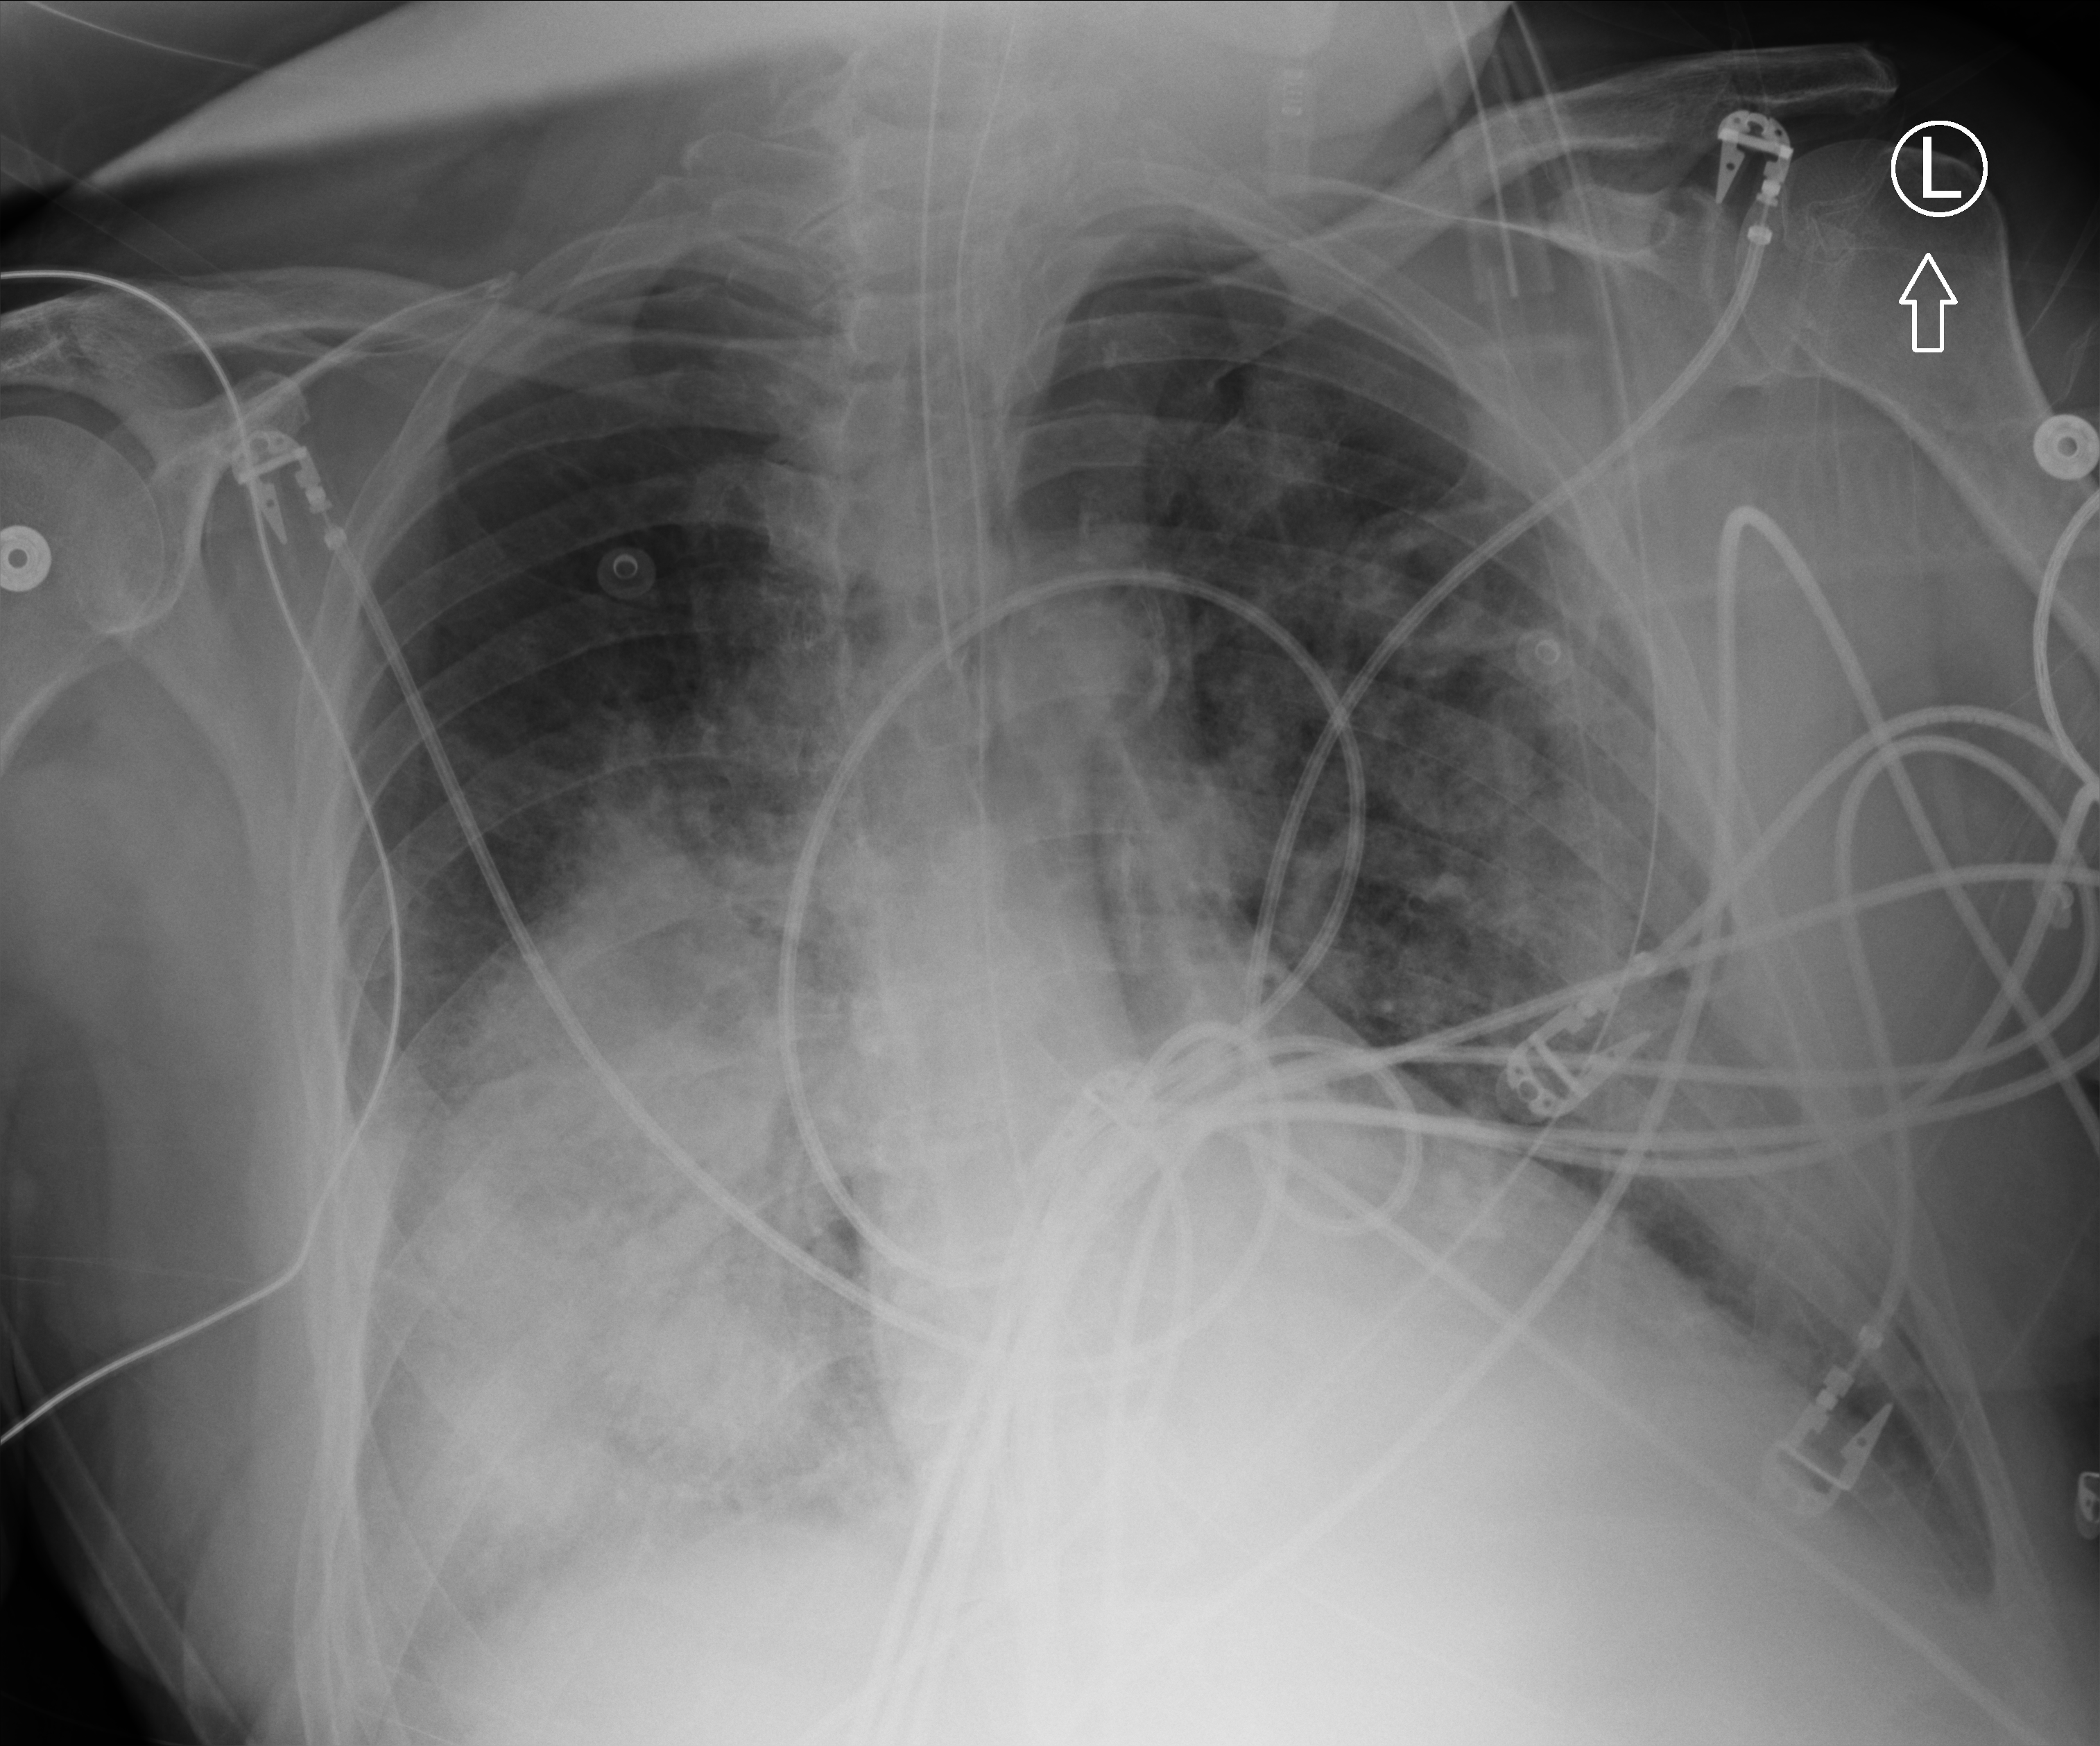
Portable chest radiograph, anteroposterior (AP) projection. Patient hospitalised with COVID-19; male, aged 60–74 years.
Hospital-stay facts (about this admission, not read from this image; timing relative to this image not recorded): admitted to intensive care during this hospital stay: yes.